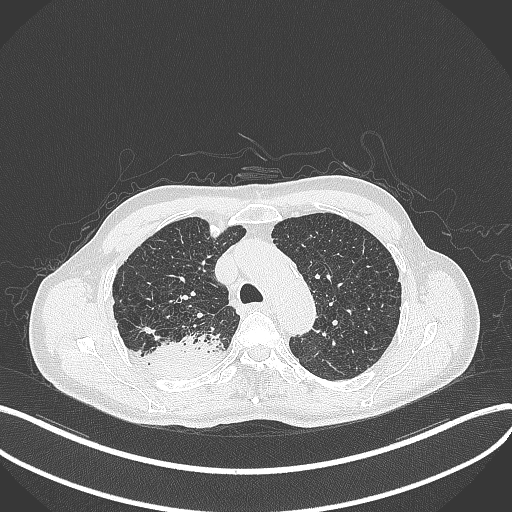
Chest CT, one axial slice. Slice 332 of 428 in the series (ordered by position). Reconstruction kernel B70f. 120 kVp. Lung window (W 1500 / L -600 HU). 1 mm slice thickness. 512 × 512 image matrix, field of view 400 × 400 mm. Patient: male, 79 years. Case-level facts recorded for this patient, not image findings: clinical TNM (as recorded): T3 N0 M0.
Outlined on this slice (bounding box drawn by a radiologist):
- lung tumour (recorded histology: adenocarcinoma): bounding box (x1, y1, x2, y2) in pixels: (139, 330, 228, 381)